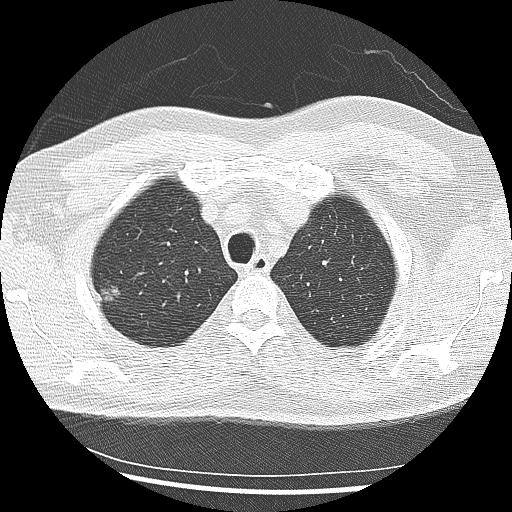
Low-dose screening chest CT, one axial slice. Position 219 of 265 along the scan axis. Reconstruction kernel LUNG. Lung window (W 1500 / L -600 HU). 2.5 mm slice thickness. 512 × 512 image matrix, field of view 340 × 340 mm.
Annotated regions visible in this slice (outlined manually by an expert reader):
- lesion 1 (tumor, upper lobe of right lung): bounding box <104,288,120,301> (left, top, right, bottom; pixels)